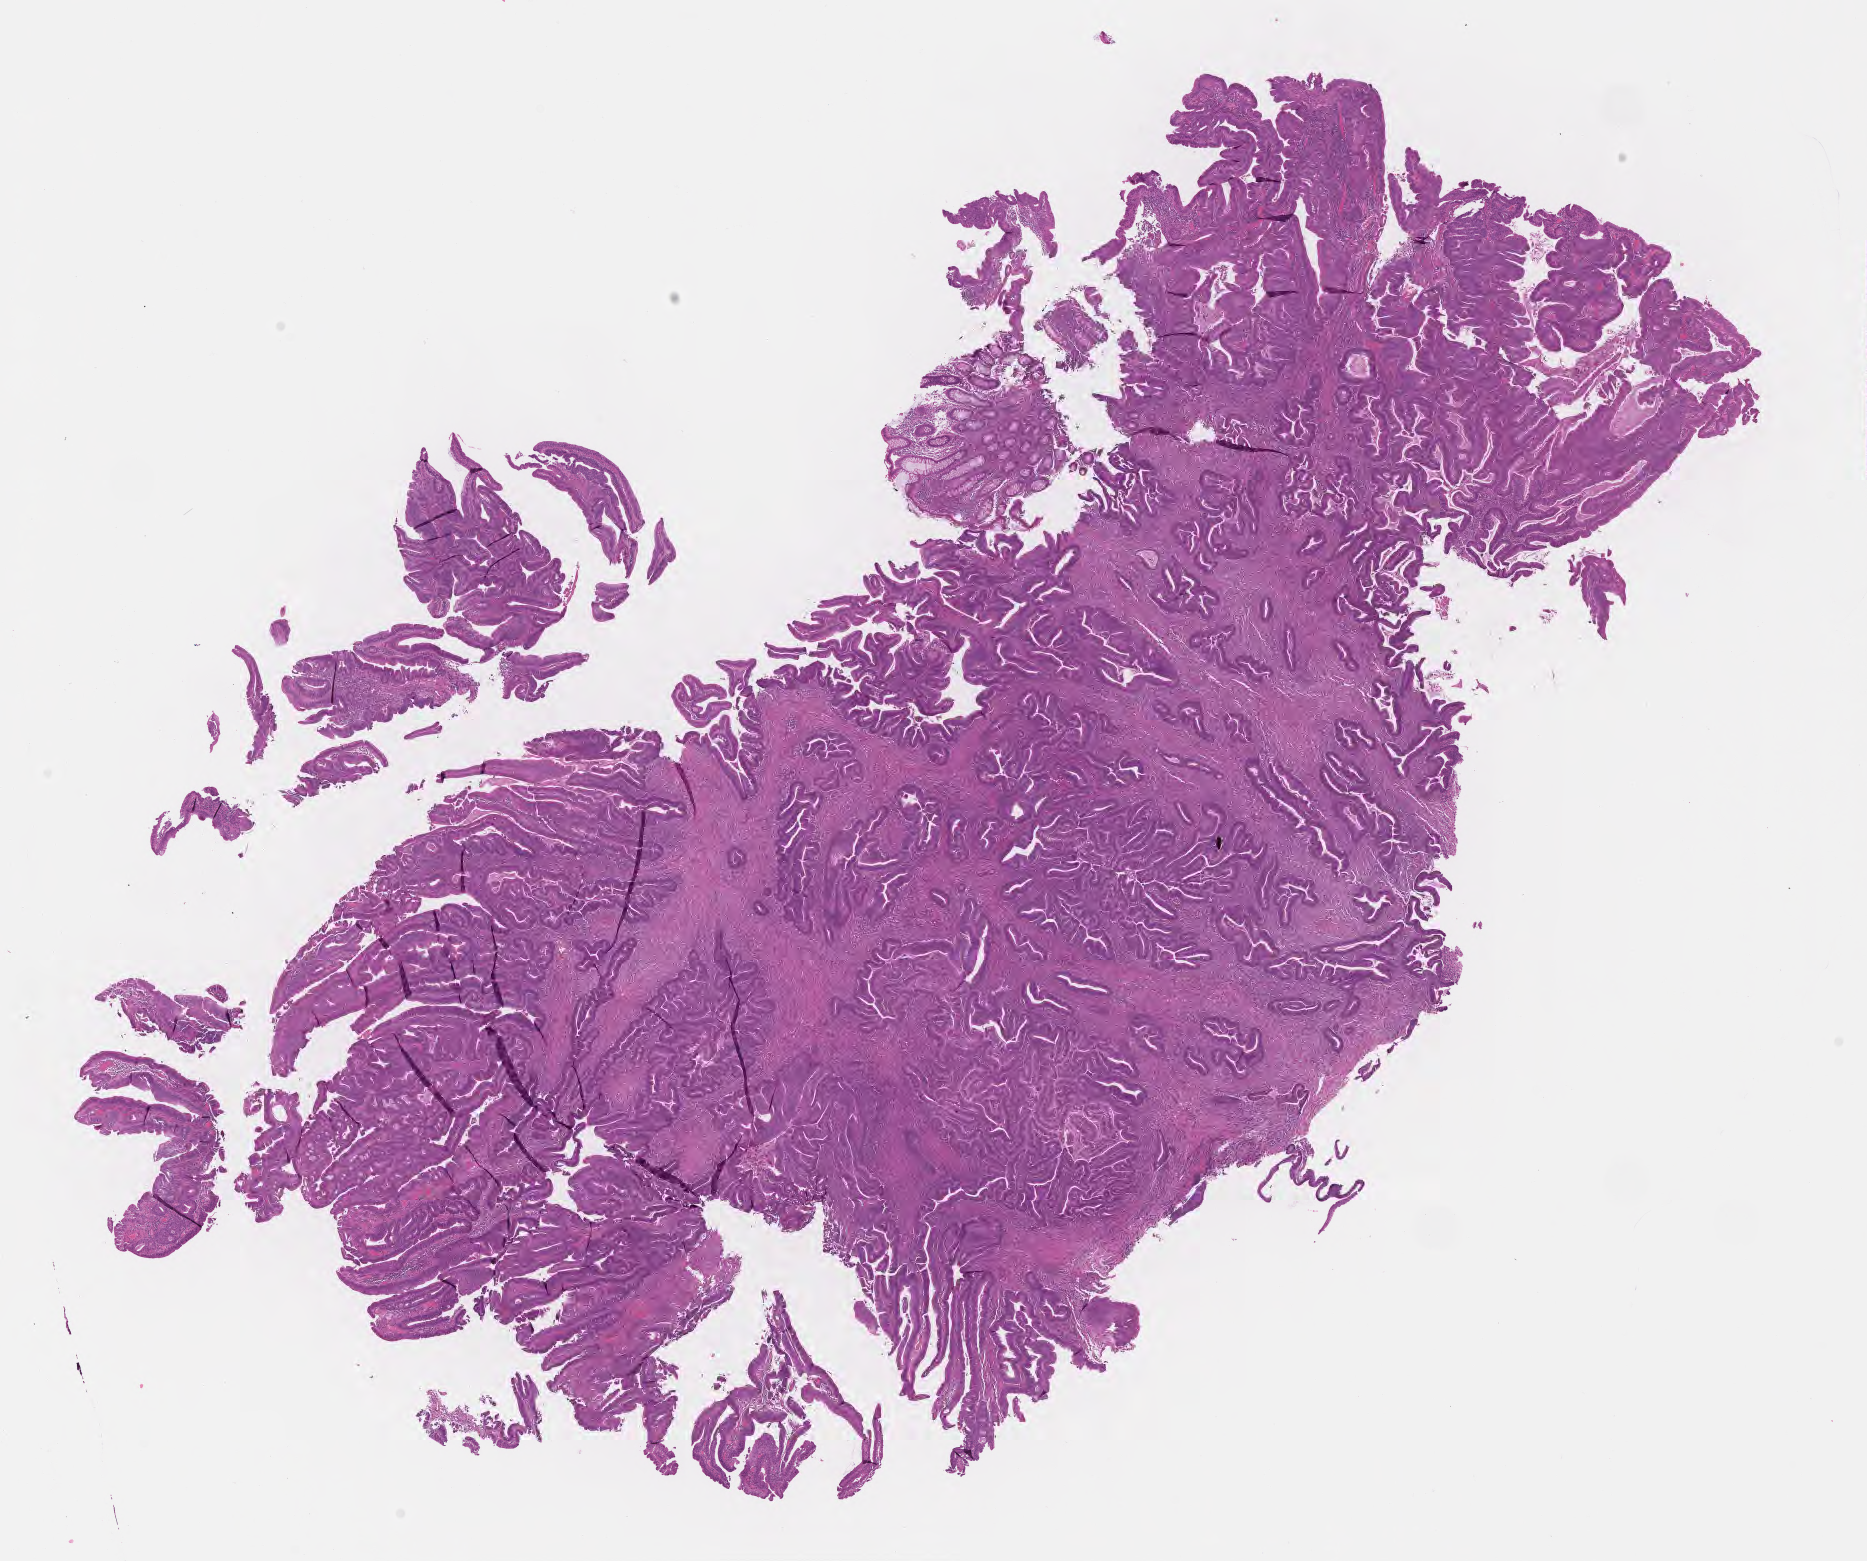
Hematoxylin and eosin (H&E) whole-slide image, whole scanned area (about 15.1 x 12.6 mm) shown as a low-resolution overview, formalin-fixed paraffin-embedded section, primary tumor, anatomic site: ascending colon. Male, age 61 years at initial diagnosis. Pathologist review of this section (percent, as recorded): tumor cells 50%, tumor nuclei 70%.
Diagnosis: Adenocarcinoma, NOS.